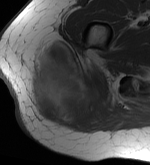
MRI of an extremity soft-tissue mass, one axial slice. Slice 18 of 56 in the series (ordered by position). MR volume resampled by the dataset authors to the PET/CT grid (not the native acquisition matrix). 3.27 mm slice thickness. 150 × 165 image matrix, field of view 146 × 161 mm. Female patient. Case-level facts recorded for this patient, not image findings: histological type: epithelioid sarcoma with vascular differentiation; site of the primary tumour: right buttock.
Outlined on this slice (expert contour drawn on MRI and transferred to this co-registered scan by the dataset authors):
- gross tumour volume (mass): bounding box (x1, y1, x2, y2) in pixels: (28, 40, 108, 128)